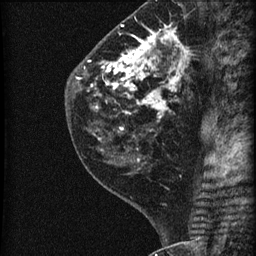
Breast MRI (dynamic contrast-enhanced), one sagittal slice; slice 26 of 60 in the series (ordered by position); dynamic contrast-enhanced series, image 2 of 3 at this slice position (ordered by acquisition); 1.5 T; TE 4.2 ms, TR 22.7 ms; 1.8 mm slice thickness; 256 × 256 image matrix. Patient: female, 45 years. Case-level facts recorded for this patient, not image findings: setting: breast cancer imaged before/during neoadjuvant chemotherapy; receptor status: HR-positive, HER2-negative.
Annotated regions visible in this slice (semi-automatically segmented with operator editing):
- analysis volume of interest (the breast-tissue region the enhancement analysis was run in; not a lesion): bounding box (x1, y1, x2, y2) in pixels: (74, 11, 205, 140)
- tumour enhancement mask (voxels above the 90 % enhancement threshold inside the analysis volume of interest): (88, 25, 190, 140)